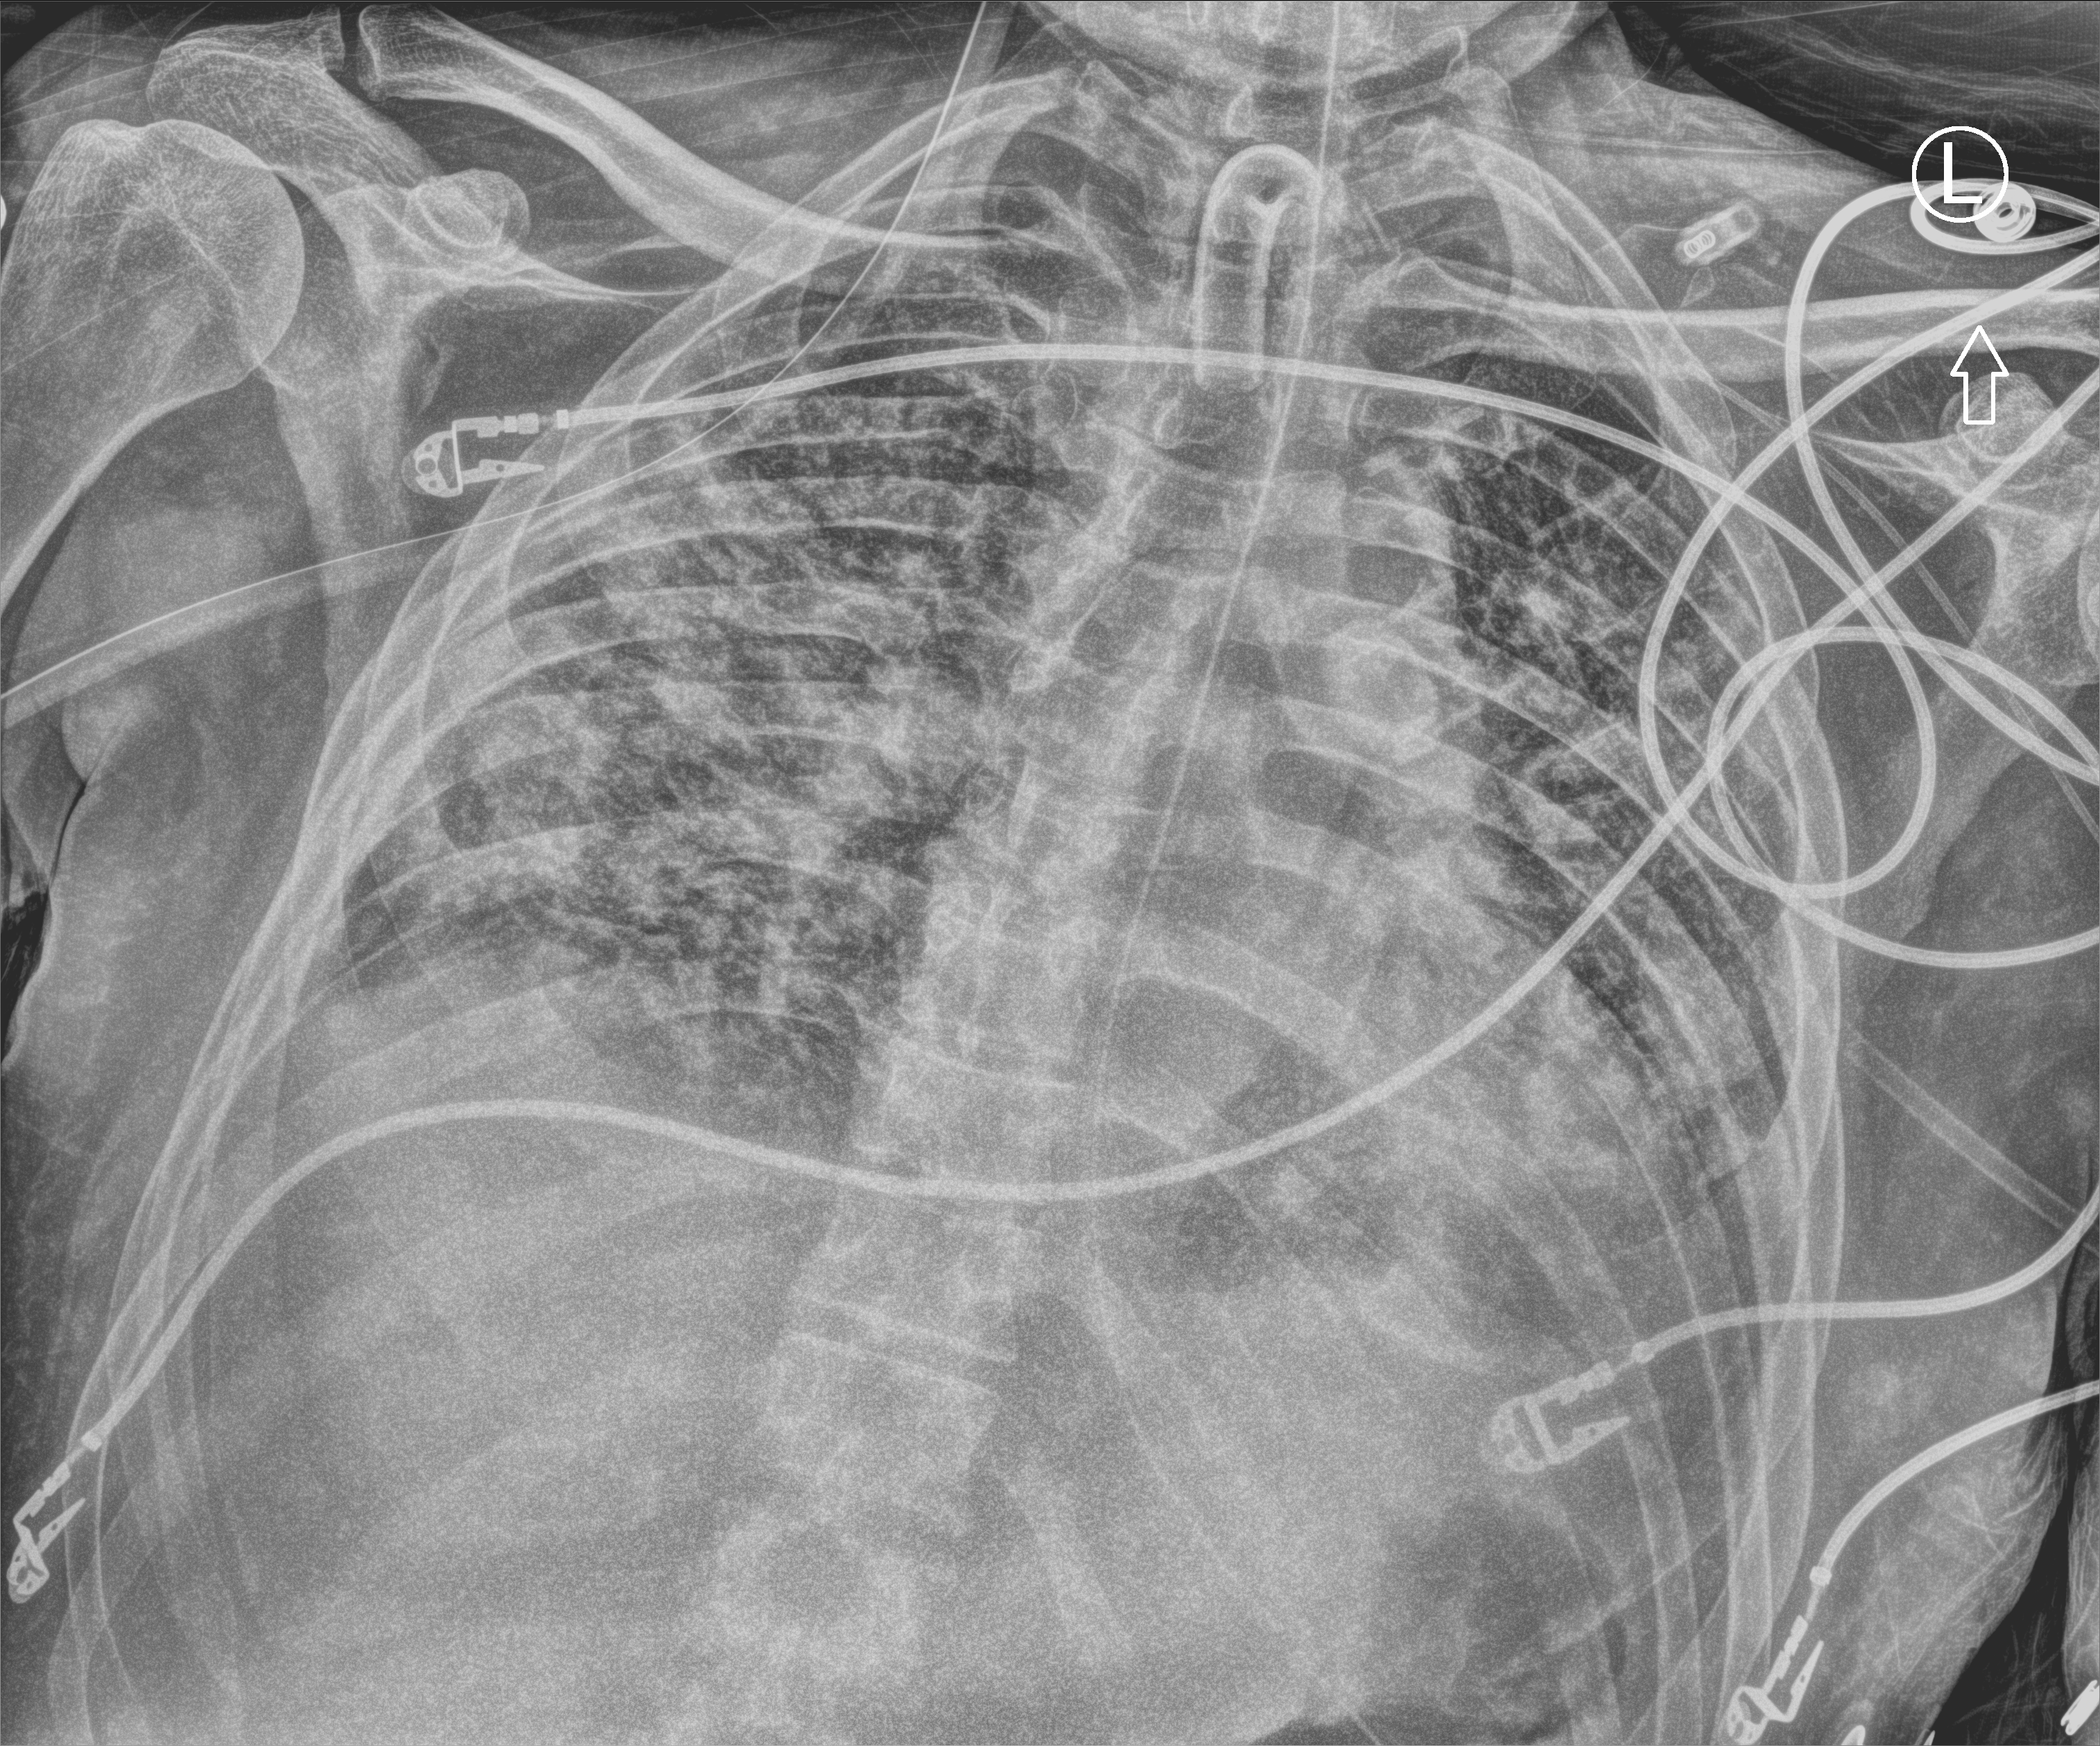
Portable chest radiograph; anteroposterior (AP) projection. Male patient hospitalised with COVID-19, age 18–59 years.
Admission-level facts for this patient (not findings on this image; timing relative to this image not recorded):
- COPD (admission record): no